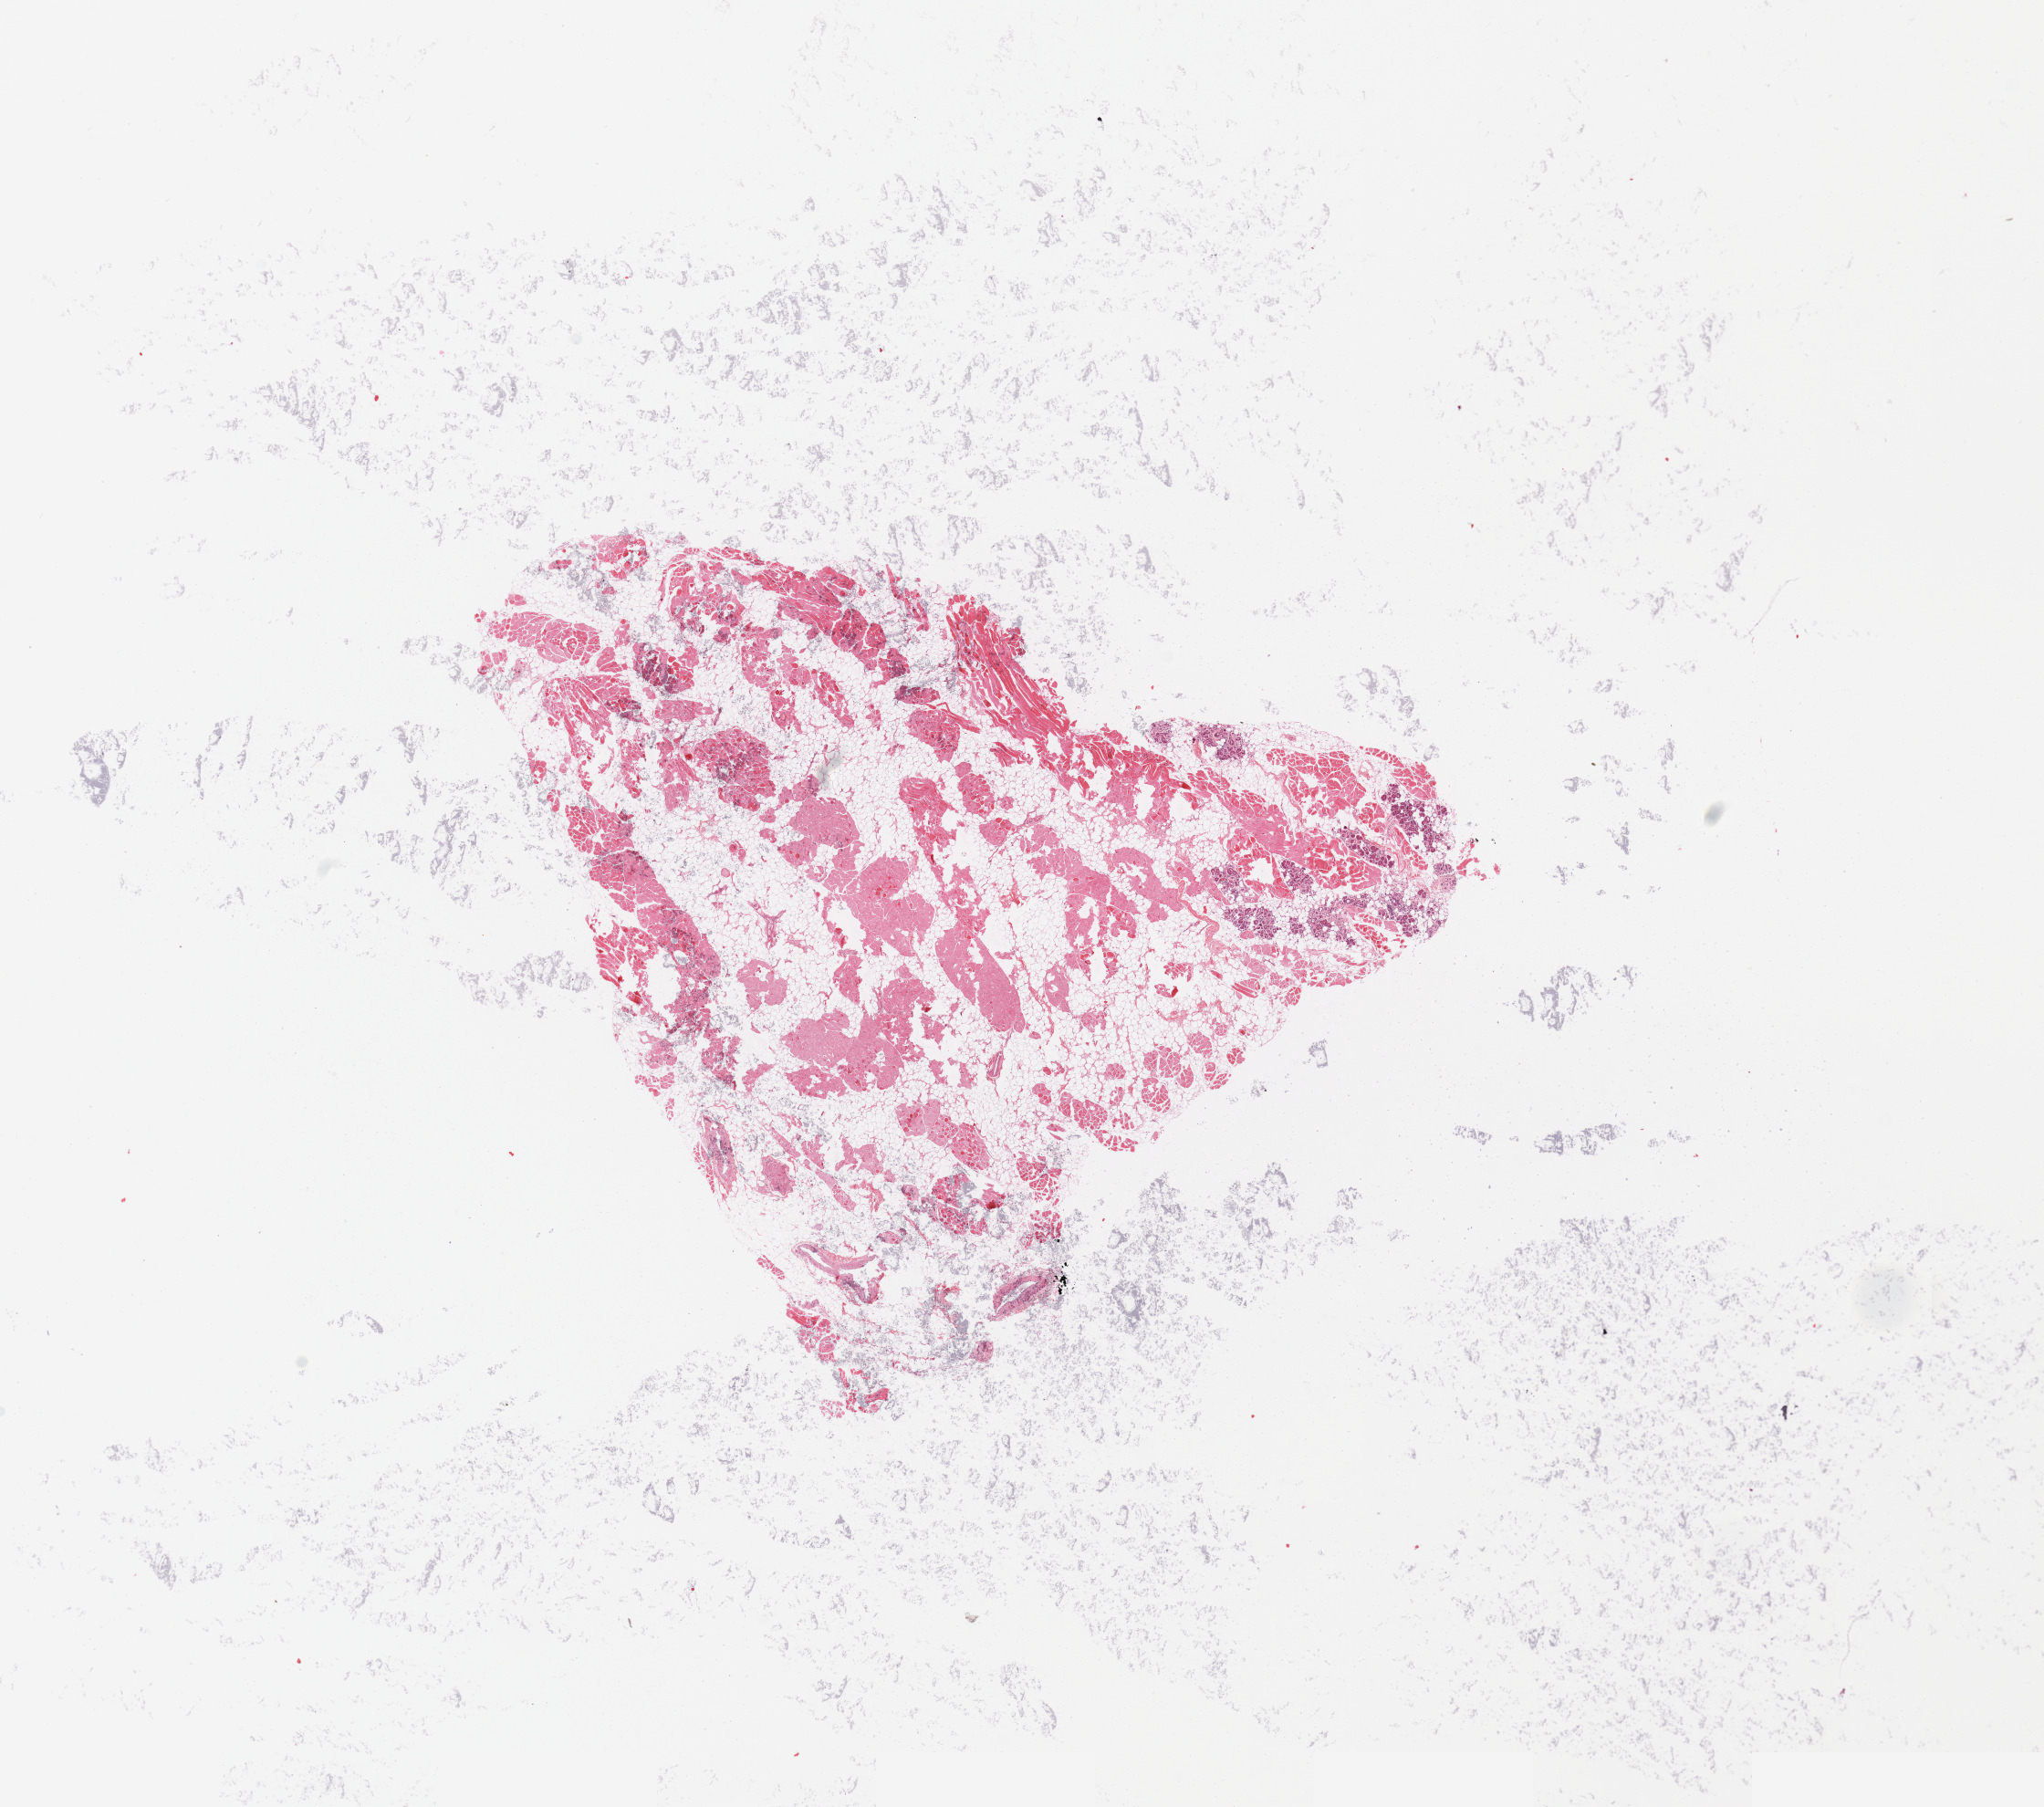
H&E whole-slide image — a low-resolution overview of the entire scanned area, about 17.7 x 15.7 mm (from a 20x scan), normal (non-tumour) tissue sample, sampled site: tongue. Female, 68 y/o.
This section: normal (non-tumour) tissue from the same patient. Patient diagnosis: Squamous cell carcinoma, NOS (tongue, NOS).